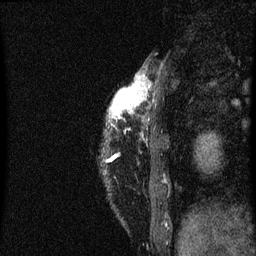
Breast MRI (dynamic contrast-enhanced), one sagittal slice; slice 11 of 60 in the series (ordered by position); dynamic contrast-enhanced series, image 2 of 3 at this slice position (ordered by acquisition); 1.5 T; TE 4.2 ms, TR 8 ms; 2 mm slice thickness; 256 × 256 image matrix, field of view 180 × 180 mm. Patient: female, 38 years.
Outlined on this slice (semi-automatically segmented with operator editing):
- analysis volume of interest (the breast-tissue region the enhancement analysis was run in; not a lesion): bounding box <110,80,145,119> (left, top, right, bottom; pixels)
- tumour enhancement mask (voxels above the 70 % enhancement threshold inside the analysis volume of interest): <112,82,143,119>